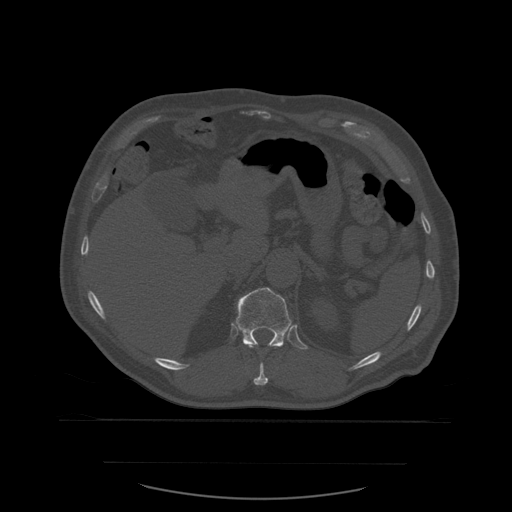
CT including the spine, one axial slice; bone window (W 1800 / L 400 HU); 1.25 mm slice thickness; 512 × 512 image matrix, field of view 479 × 479 mm. Patient age 71 years. Case-level facts recorded for this patient, not image findings: primary cancer: lung; vertebrae with lytic lesions (as recorded): T1, T2, L5, S1.
Structures marked on this image (semi-automatic segmentation, software-assisted and operator-edited):
- T11 vertebra: bounding box [x1, y1, x2, y2] px = [254, 363, 269, 386]
- T12 vertebra: [236, 288, 292, 349]